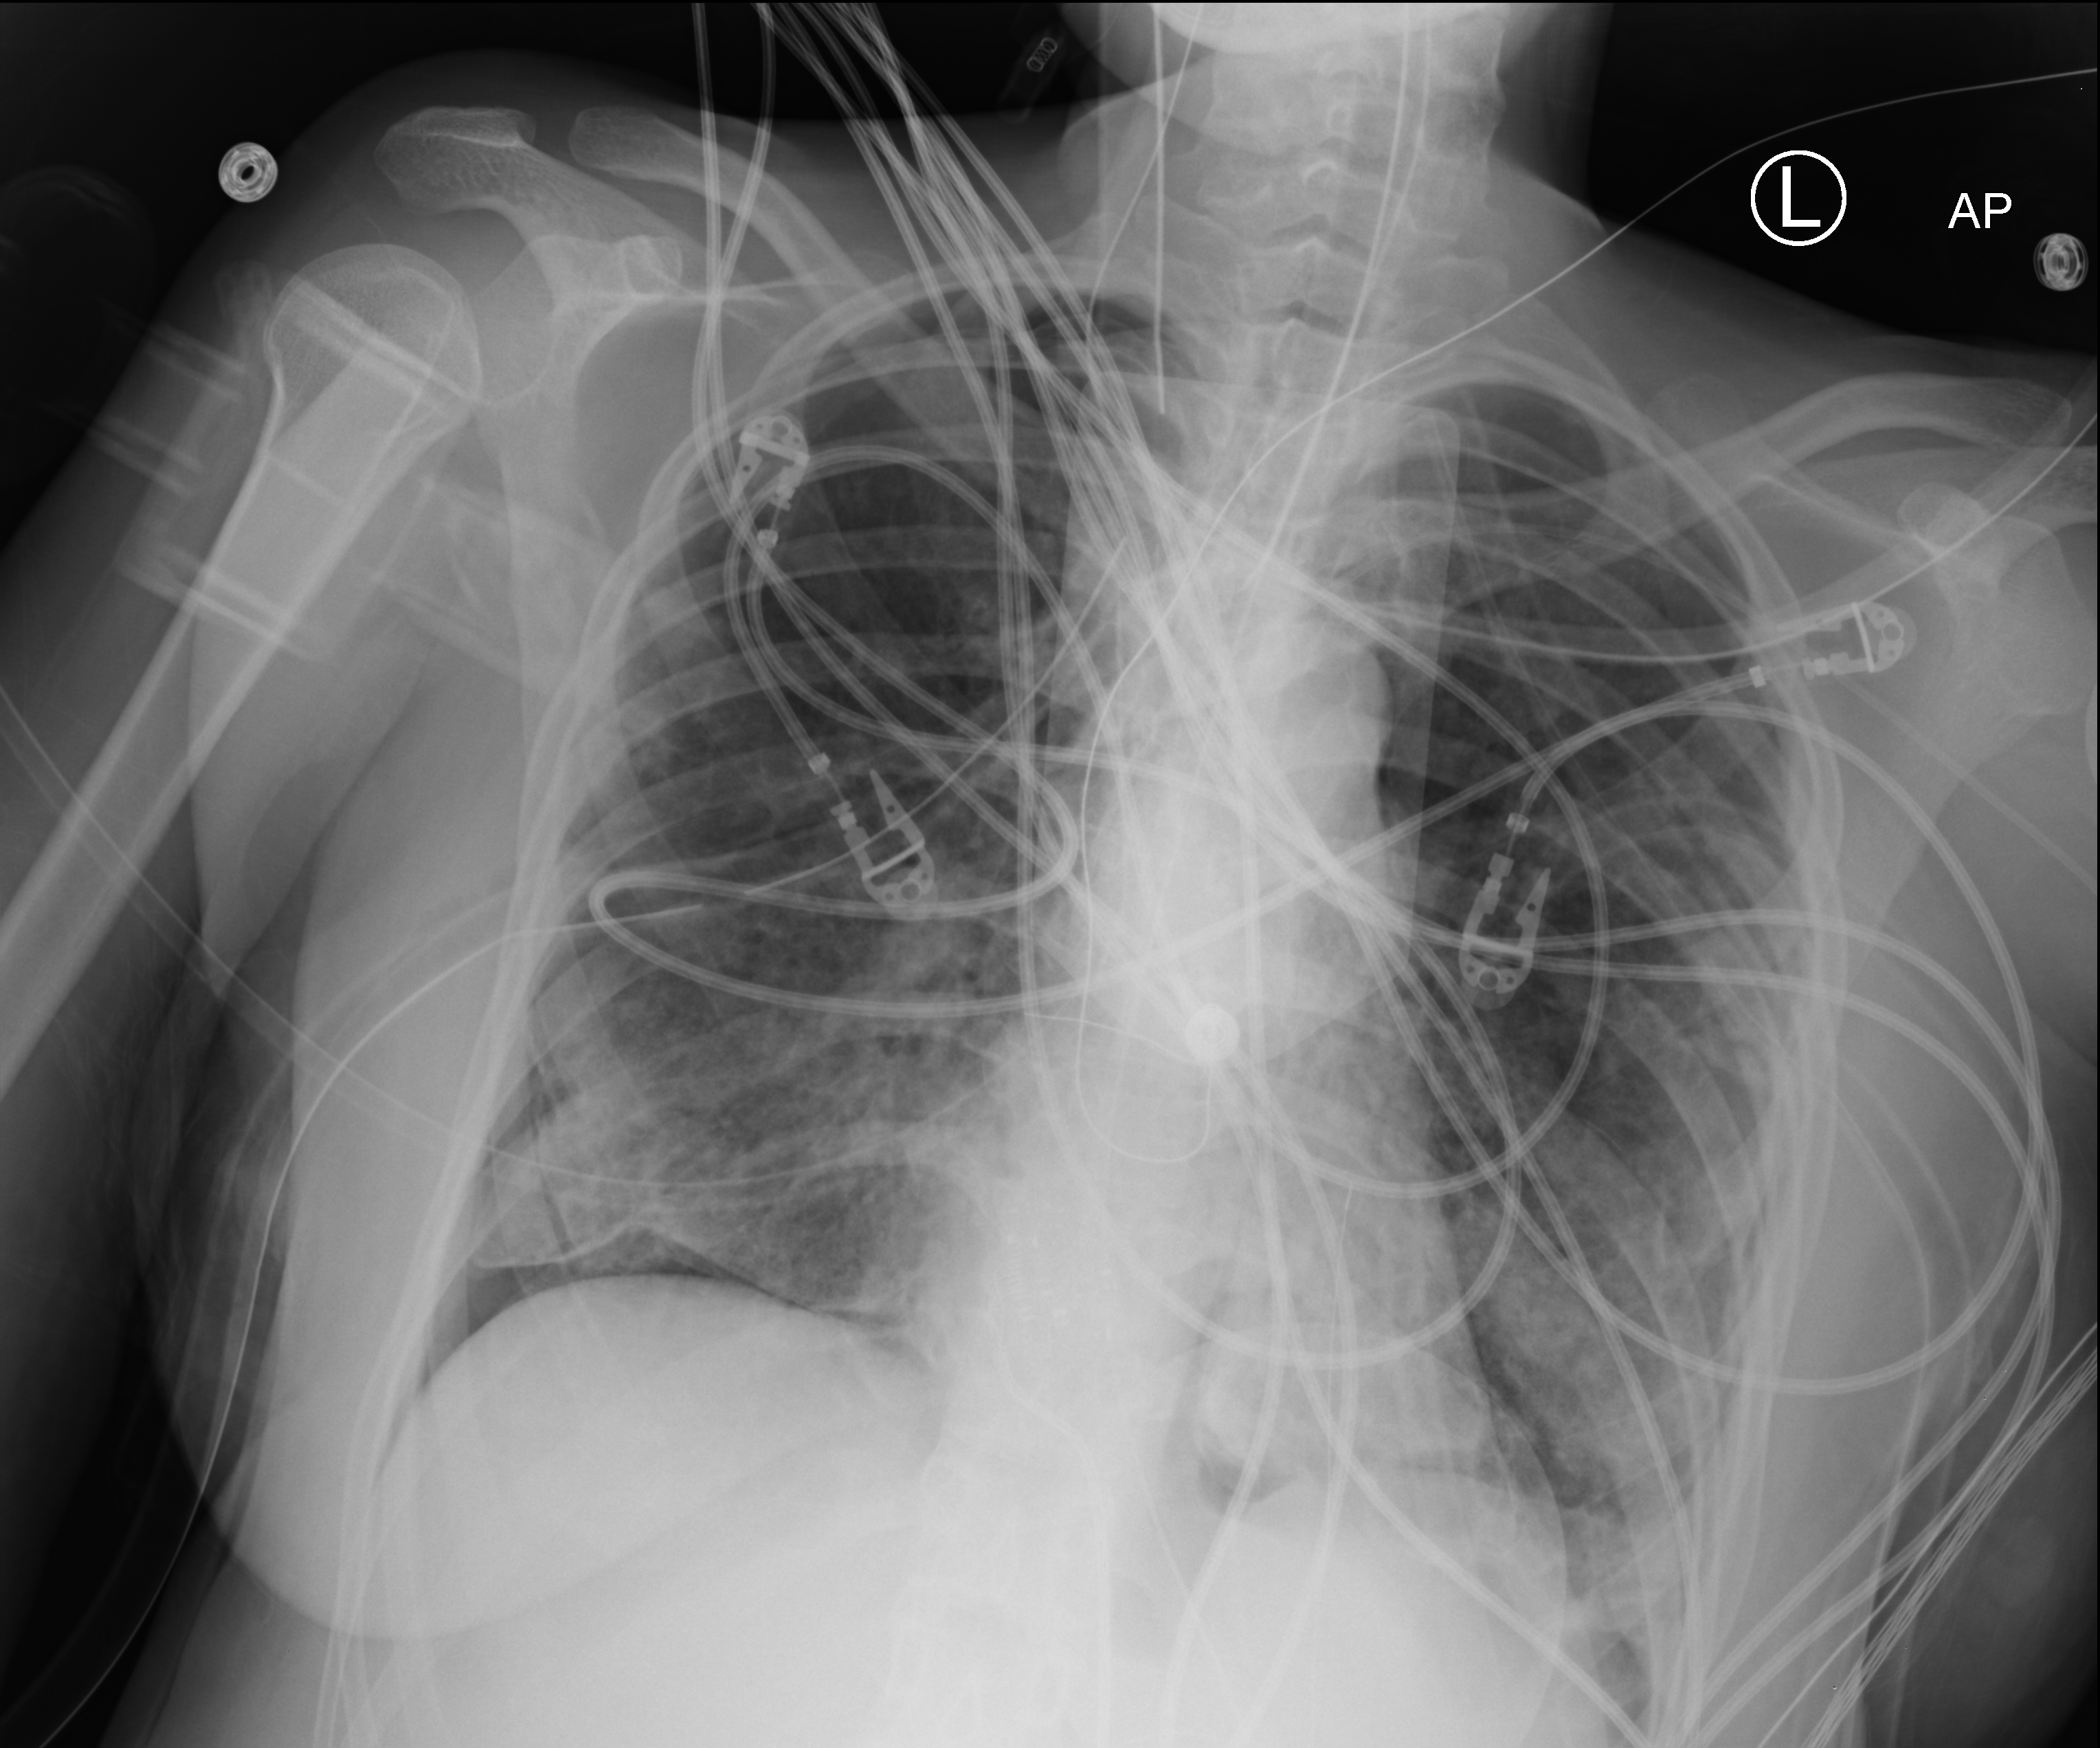
Chest X-ray (portable); anteroposterior (AP) projection. Patient hospitalised with COVID-19, aged 18–59 years.
Hospital-stay facts (about this admission, not read from this image; timing relative to this image not recorded):
- admitted to intensive care during this hospital stay: yes